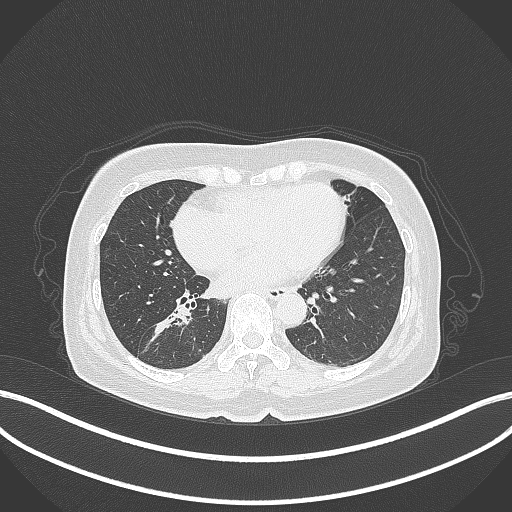
Chest CT, one axial slice. Position 158 of 429 along the scan axis. Reconstruction kernel B70f. 120 kVp. Lung window (W 1500 / L -600 HU). 1 mm slice thickness. 512 × 512 image matrix. Patient: female, 67 years. Case-level facts recorded for this patient, not image findings: clinical TNM (as recorded): T1c N1 M0.
Structures marked on this image (rectangle marked by the reading radiologist):
- lung tumour (recorded histology: adenocarcinoma): bounding box <141,303,192,356> (left, top, right, bottom; pixels)